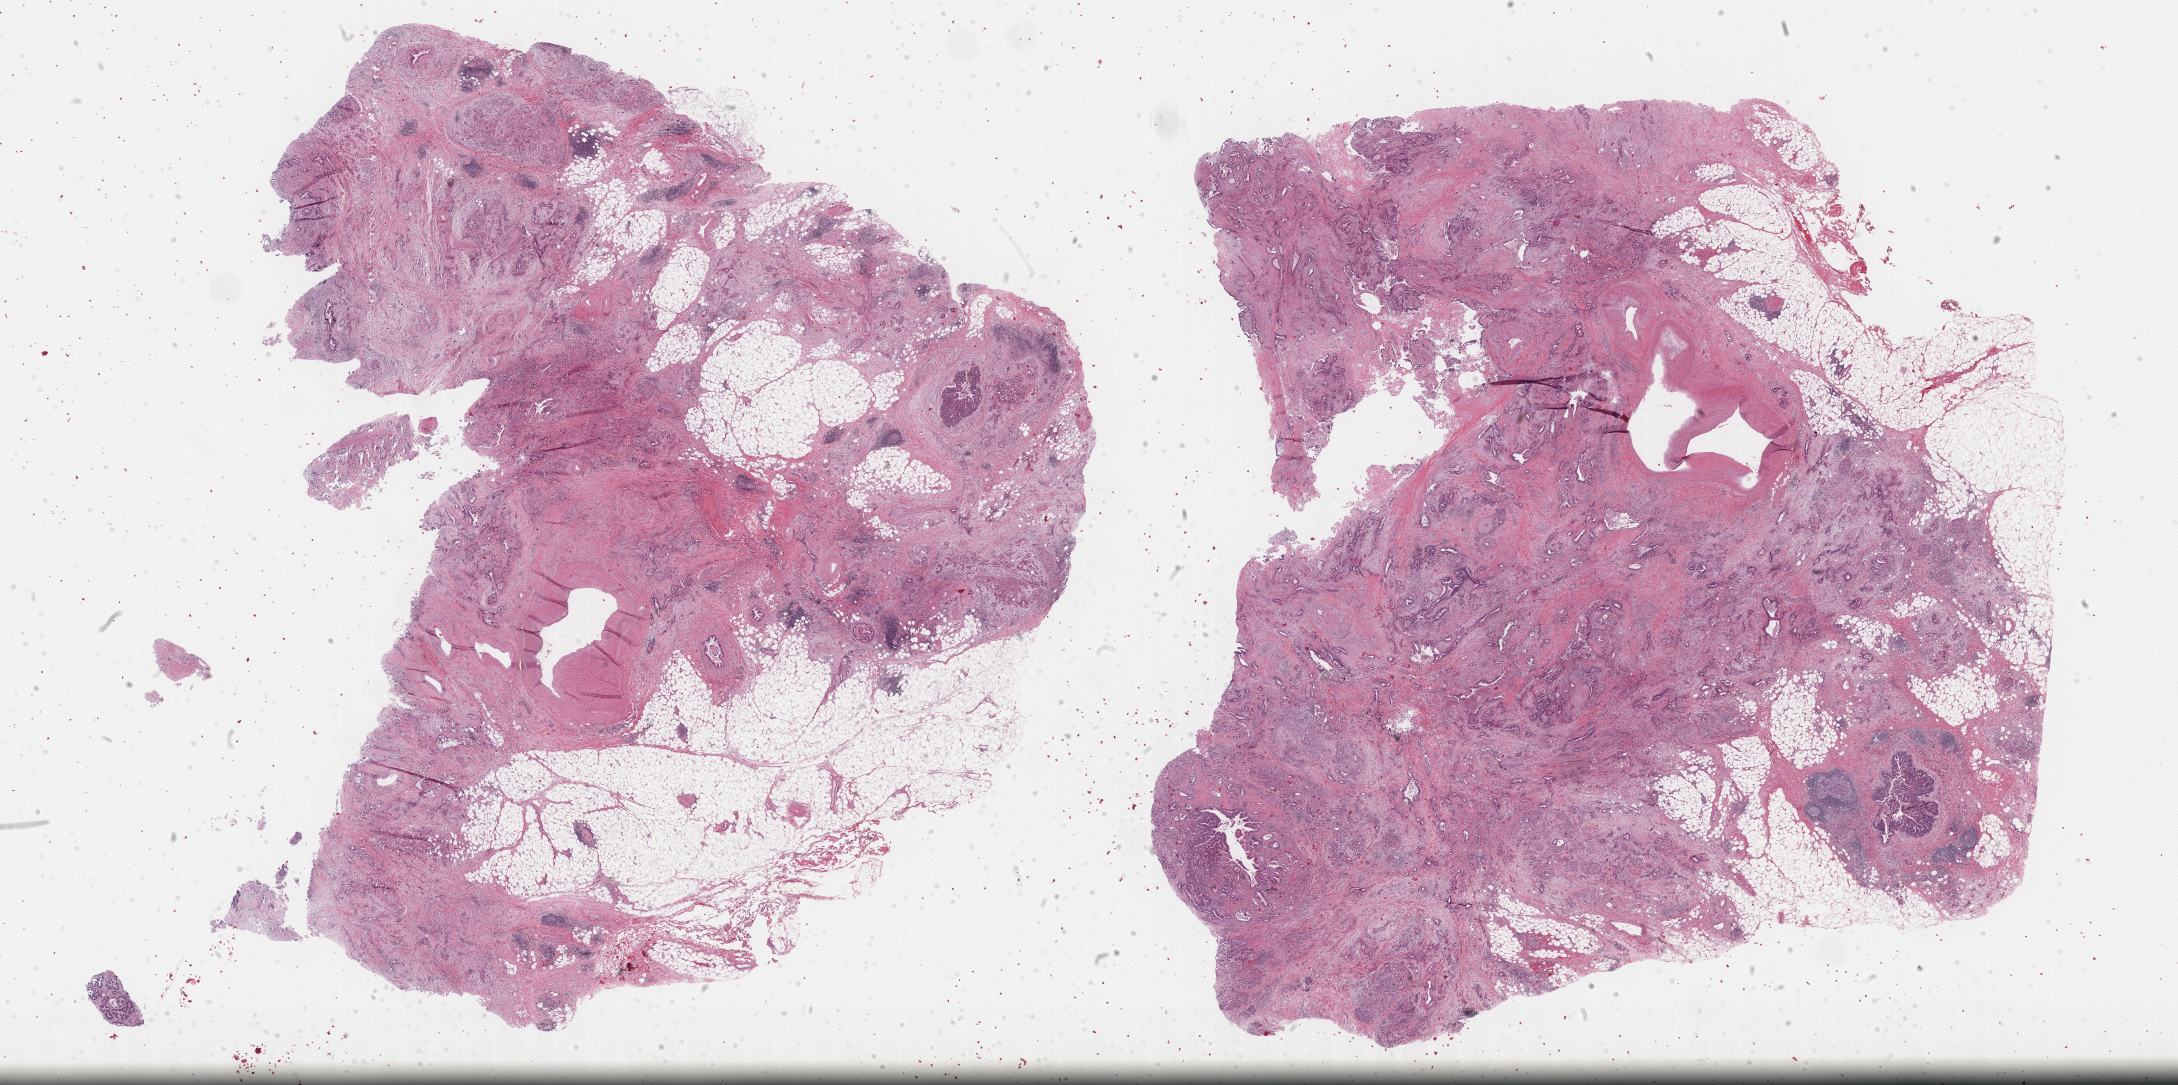
Whole-slide histology image, Hematoxylin and eosin (H&E) stained, whole scanned area (about 35.2 x 17.6 mm) shown as a low-resolution overview. Formalin-fixed paraffin-embedded (FFPE) diagnostic section. Sample: primary tumour, pancreas. Male patient; age at initial diagnosis 73 years. Histologic grade: G3 (poorly differentiated).
Lymph nodes positive (case pathology): 4 of 18 examined. AJCC pathologic stage: IIB (7th edition). Pathologic diagnosis: Infiltrating duct carcinoma, NOS (head of pancreas).